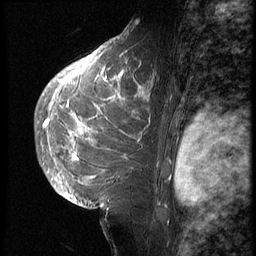
Breast MRI (dynamic contrast-enhanced), one sagittal slice; slice 39 of 62 in the series (ordered by position); 3 images stored at this slice position (order not interpretable as contrast timing); 1.5 T; TE 4.2 ms, TR 9 ms; 2.5 mm slice thickness; 256 × 256 image matrix. Patient: female, 28 years. From the clinical record (not read from this slice): setting: breast cancer imaged before/during neoadjuvant chemotherapy.
Annotated regions visible in this slice (semi-automatic segmentation, software-assisted and operator-edited):
- analysis volume of interest (the breast-tissue region the enhancement analysis was run in; not a lesion): bounding box [x1, y1, x2, y2] px = [42, 45, 159, 207]
- tumour enhancement mask (voxels above the 140 % enhancement threshold inside the analysis volume of interest): [43, 51, 143, 178]